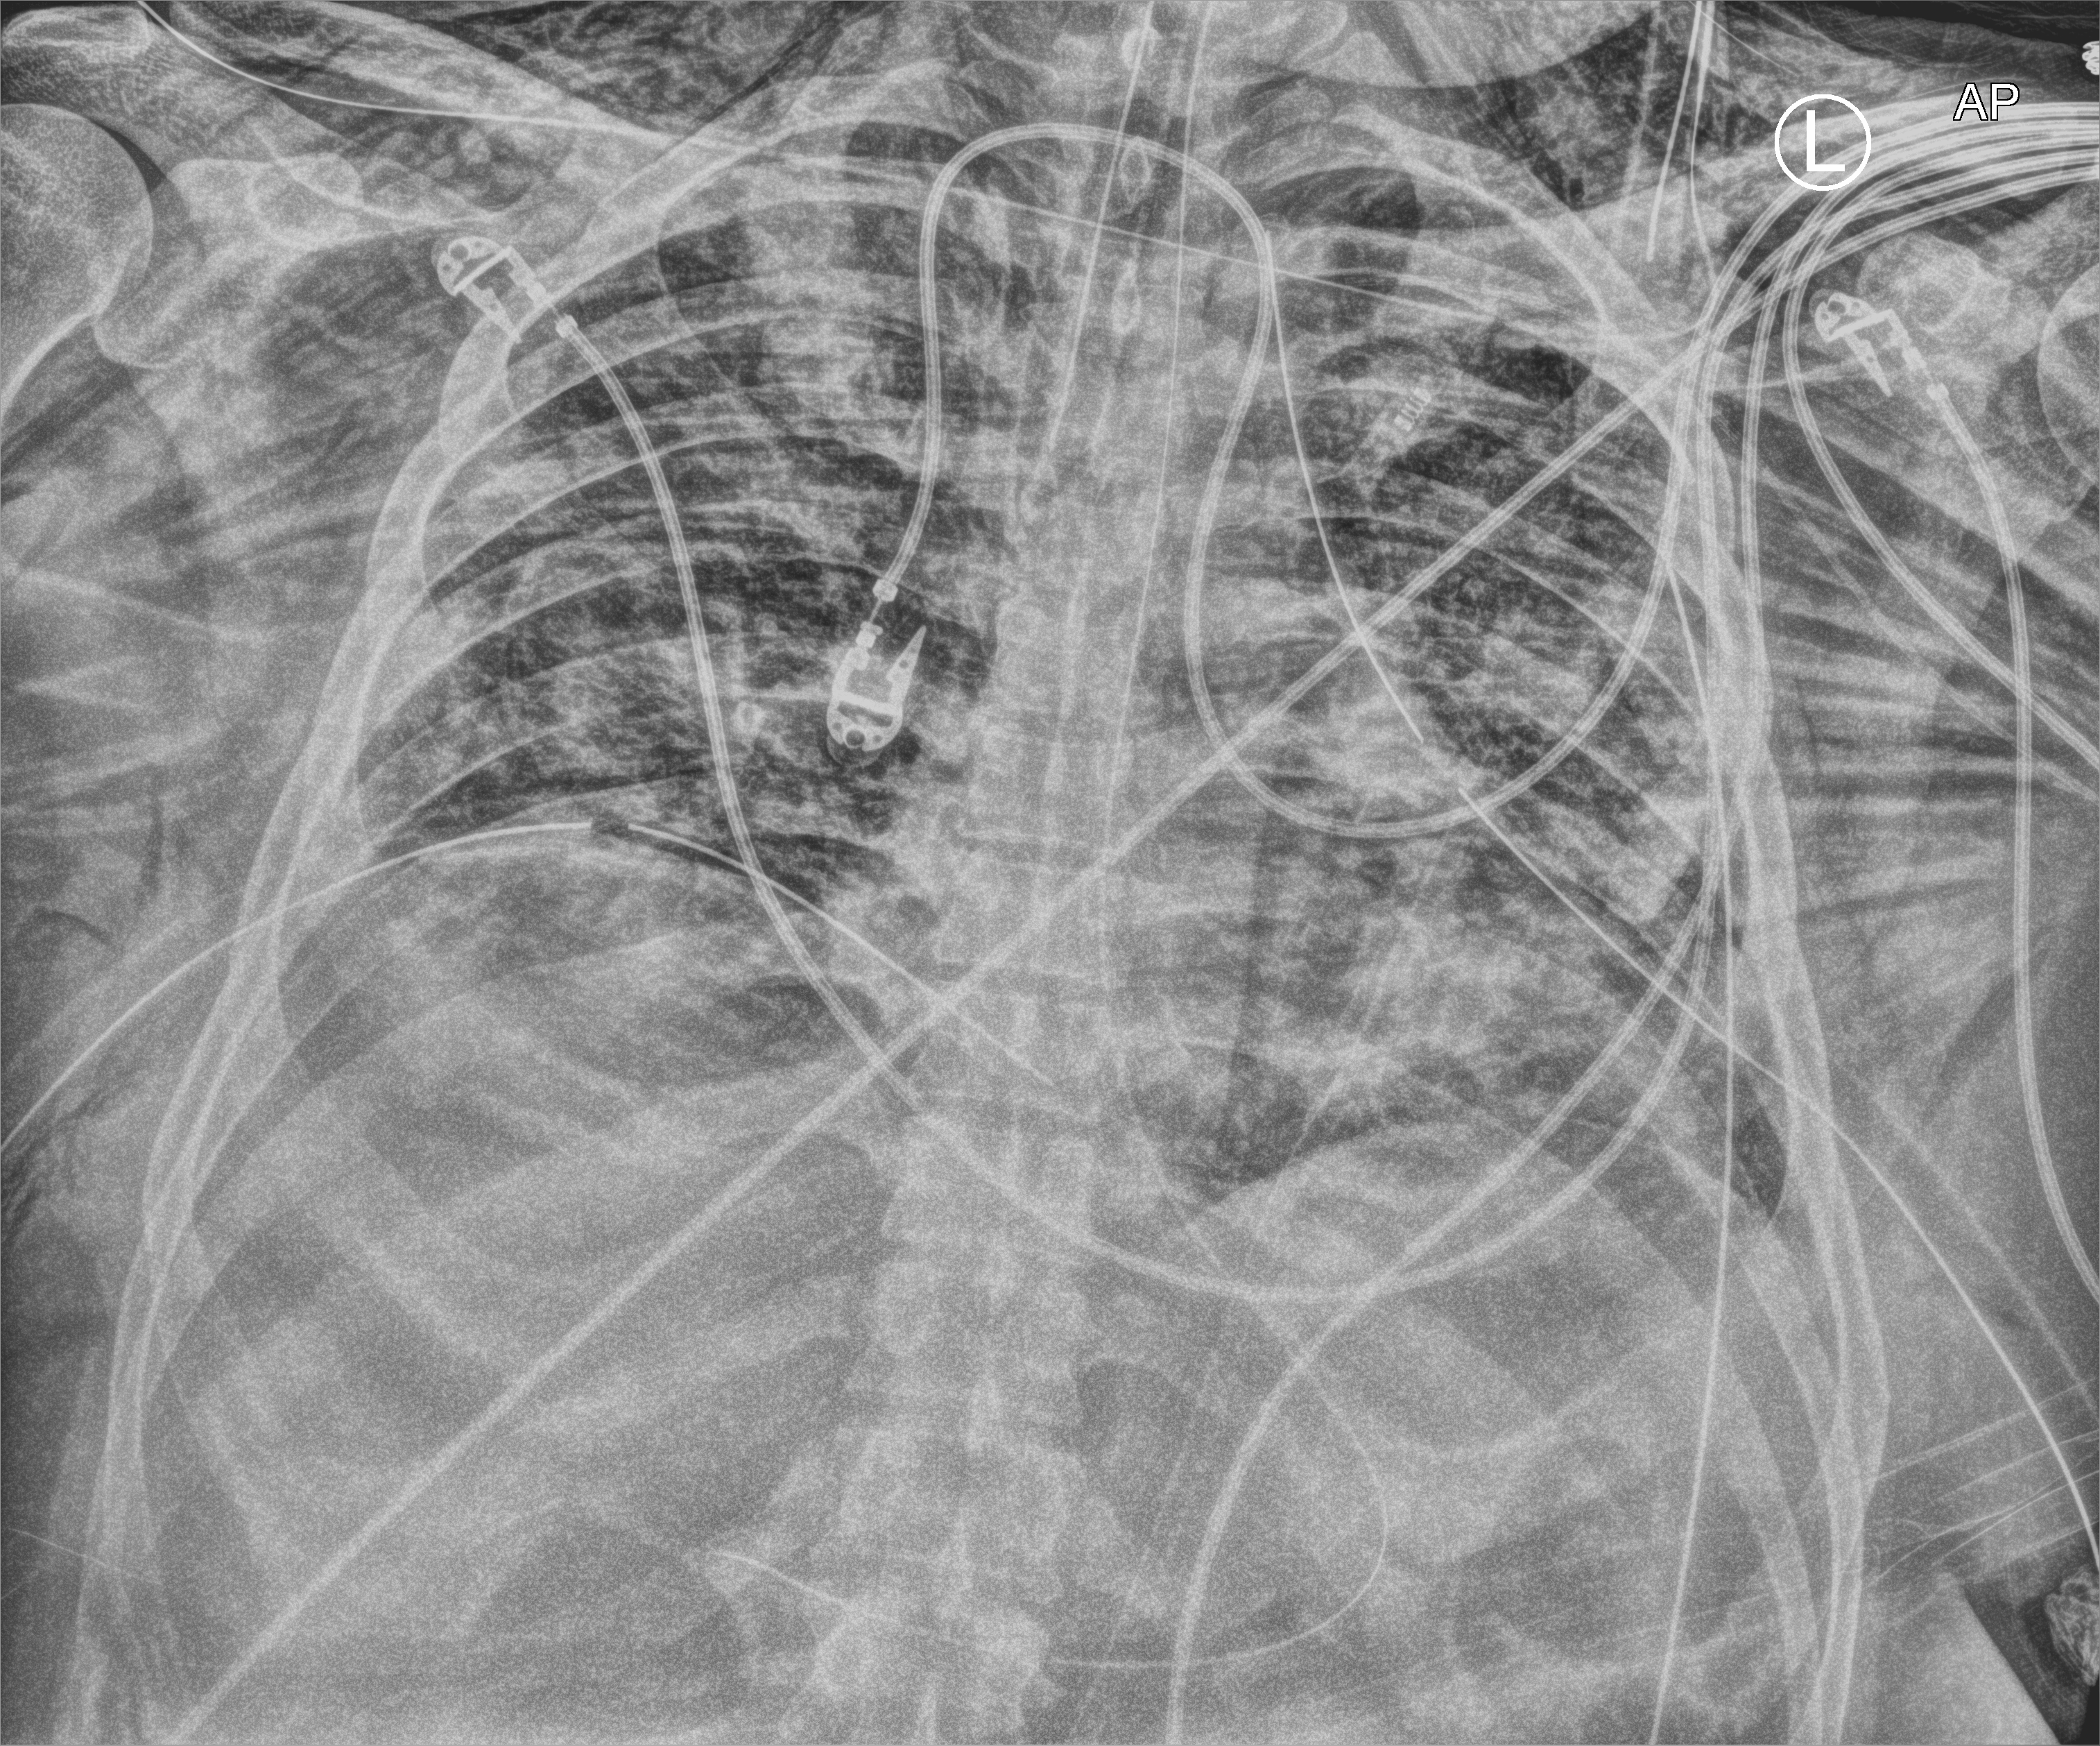
Portable chest radiograph; anteroposterior (AP) projection. Male patient hospitalised with COVID-19, age 18–59 years.
Admission-level facts for this patient (not findings on this image; timing relative to this image not recorded): admitted to intensive care during this hospital stay: yes.